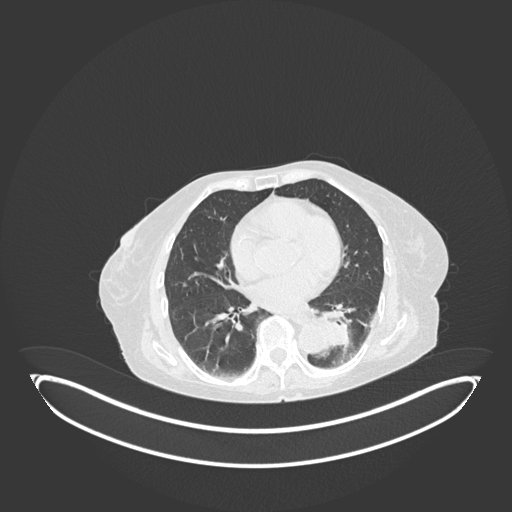
Chest CT, one axial slice; slice 47 of 189 in the series (ordered by position); reconstruction kernel B30f; 120 kVp; lung window (W 1500 / L -600 HU); 1 mm slice thickness; 512 × 512 image matrix, field of view 500 × 500 mm. Female patient, age 82 years. From the clinical record (not read from this slice): clinical TNM (as recorded): T1b N0 M1.
Structures marked on this image (bounding box drawn by a radiologist):
- lung tumour (recorded histology: adenocarcinoma): bounding box <316,312,356,355> (left, top, right, bottom; pixels)